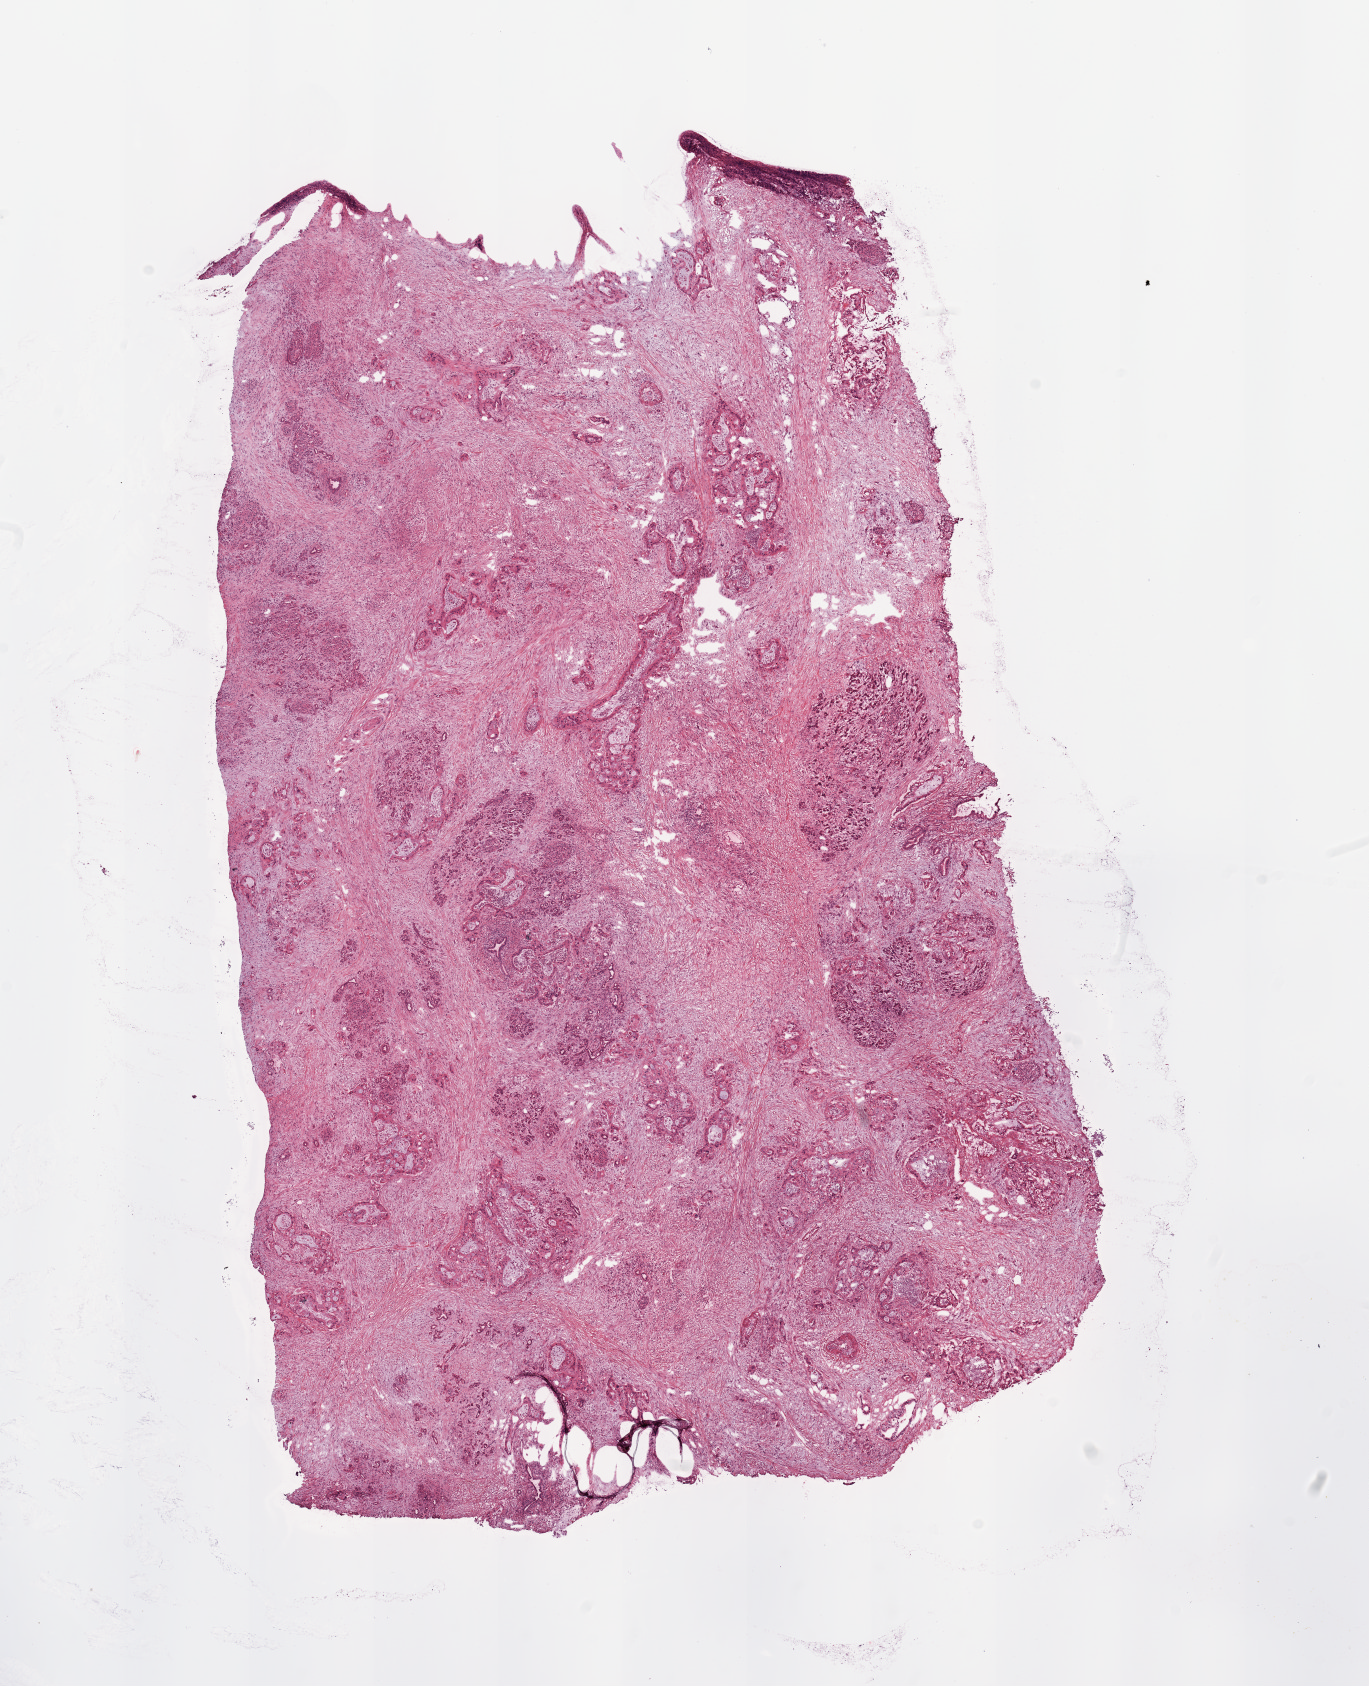
Whole-slide histology image, Hematoxylin and eosin (H&E) stained, a low-resolution overview of the entire scanned area, about 10.8 x 13.3 mm; tumour tissue sample, sampled site: pancreas. Patient: female, age 62 years.
Histologic diagnosis: Infiltrating duct carcinoma, NOS.